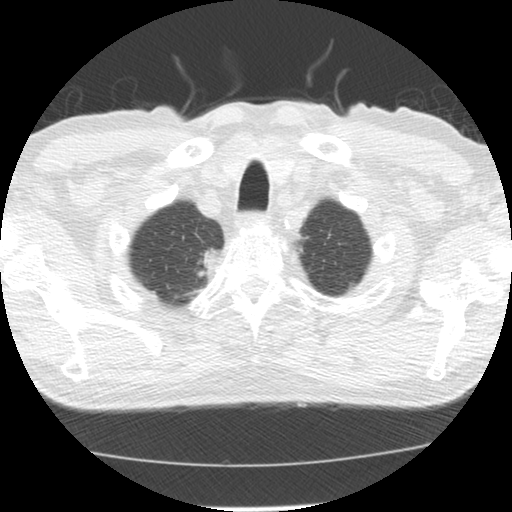
Low-dose screening chest CT, axial slice, baseline screening round, lung window (W 1500 / L -600 HU). Male participant, aged 64 years at enrolment. Former smoker at enrolment.
• Expert reader's lesion annotation, bounding box [x1, y1, x2, y2] px = [182, 243, 225, 284].
• Screening reader's record for this exam (one nodule recorded; not confirmed to be the boxed lesion): non-calcified nodule or mass ≥4 mm, right upper lobe, 20 × 13 mm, spiculated (stellate) margins, soft tissue attenuation.
• Official screen result: positive, change unspecified: nodule(s) >= 4 mm or enlarging nodule(s), mass(es), or other non-specific abnormalities suspicious for lung cancer.